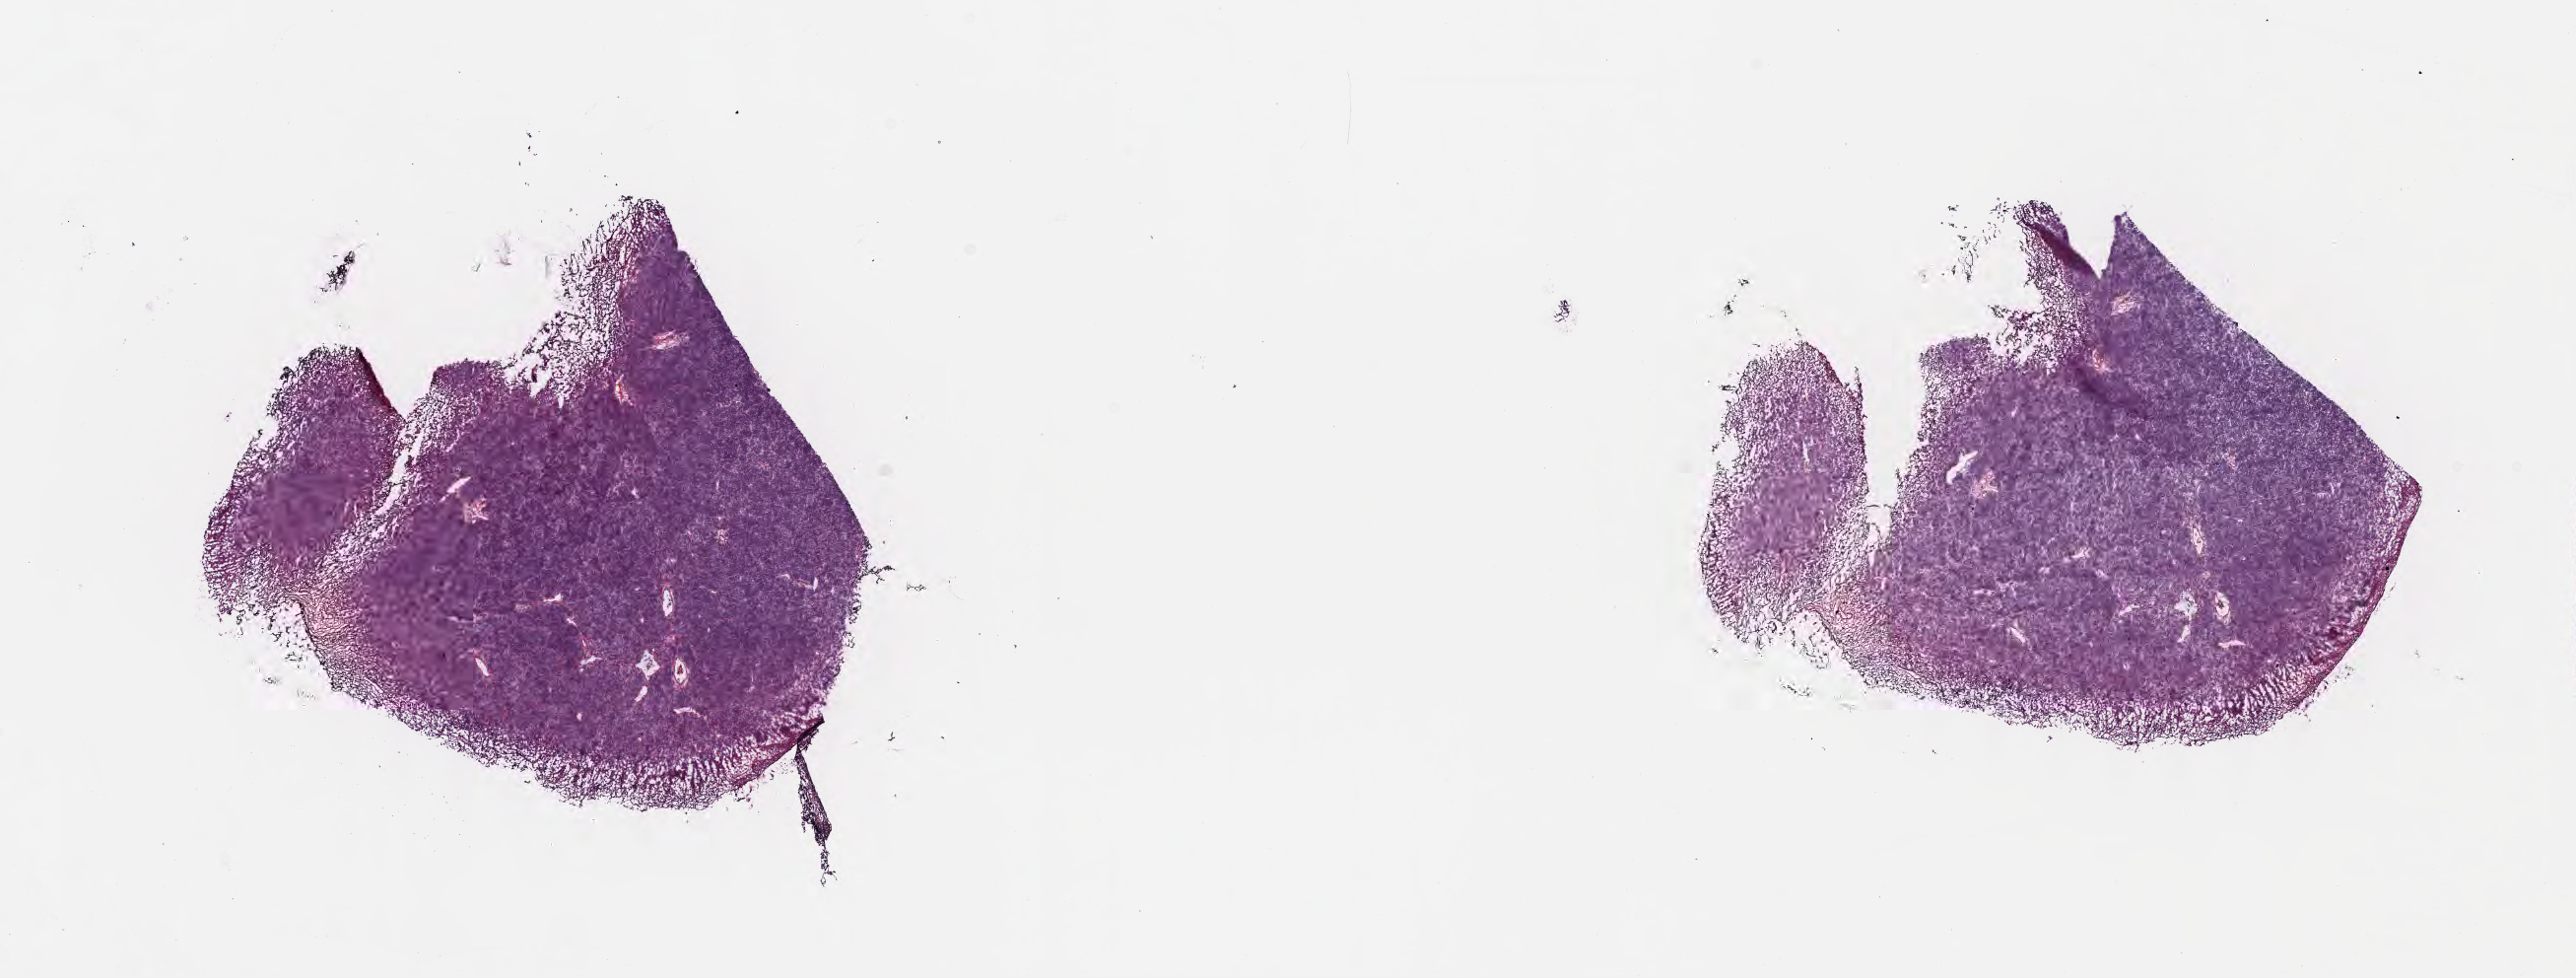
Whole-slide image, haematoxylin and eosin stain — whole scanned area (about 21.1 x 8.0 mm) shown as a low-resolution overview; frozen section; specimen: primary tumor; anatomic site: mandible. Male, age 6 years at initial diagnosis. Slide review estimates, as recorded: tumor cells 90%, tumor nuclei 90%, stromal cells 5%, necrosis 5%, normal cells 0%. Infiltration values recorded for this section: lymphocyte infiltration 60%, monocyte infiltration 20%, neutrophil infiltration 0%.
Histologic diagnosis: Diffuse large B-cell lymphoma, NOS. Ann Arbor stage (patient): Stage IV.